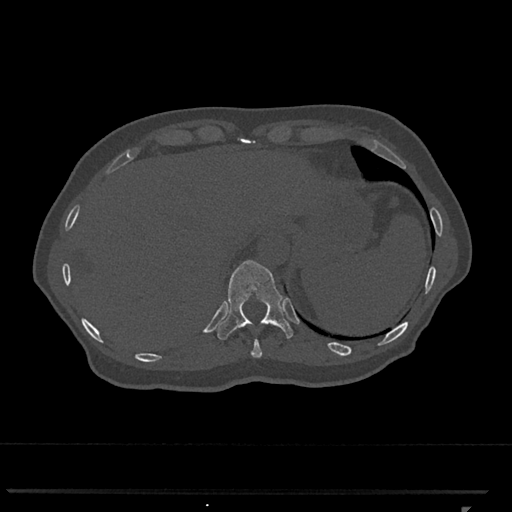
CT including the spine, one axial slice; position 531 of 793 along the scan axis; reconstruction kernel Br40s/3; 120 kVp; bone window (W 1800 / L 400 HU); 512 × 512 image matrix, field of view 380 × 380 mm. Patient: female, 62 years. From the clinical record (not read from this slice): primary cancer: renal.
Structures marked on this image (semi-automatically segmented with operator editing):
- T10 vertebra: bounding box [x1, y1, x2, y2] px = [251, 339, 262, 358]
- T11 vertebra: [217, 260, 293, 340]